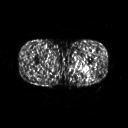
FDG PET of an extremity soft-tissue mass (from a PET/CT study), one axial slice. Position 237 of 267 along the scan axis. 3.27 mm slice thickness. 128 × 128 image matrix, field of view 500 × 500 mm. Male patient, age 27 years. Case-level facts recorded for this patient, not image findings: histological type: extraskeletal osteosarcoma; grade: high; site of the primary tumour: left adductur.
Annotated regions visible in this slice (expert contour drawn on MRI and transferred to this co-registered scan by the dataset authors):
- gross tumour volume (mass): bounding box <68,61,95,74> (left, top, right, bottom; pixels)